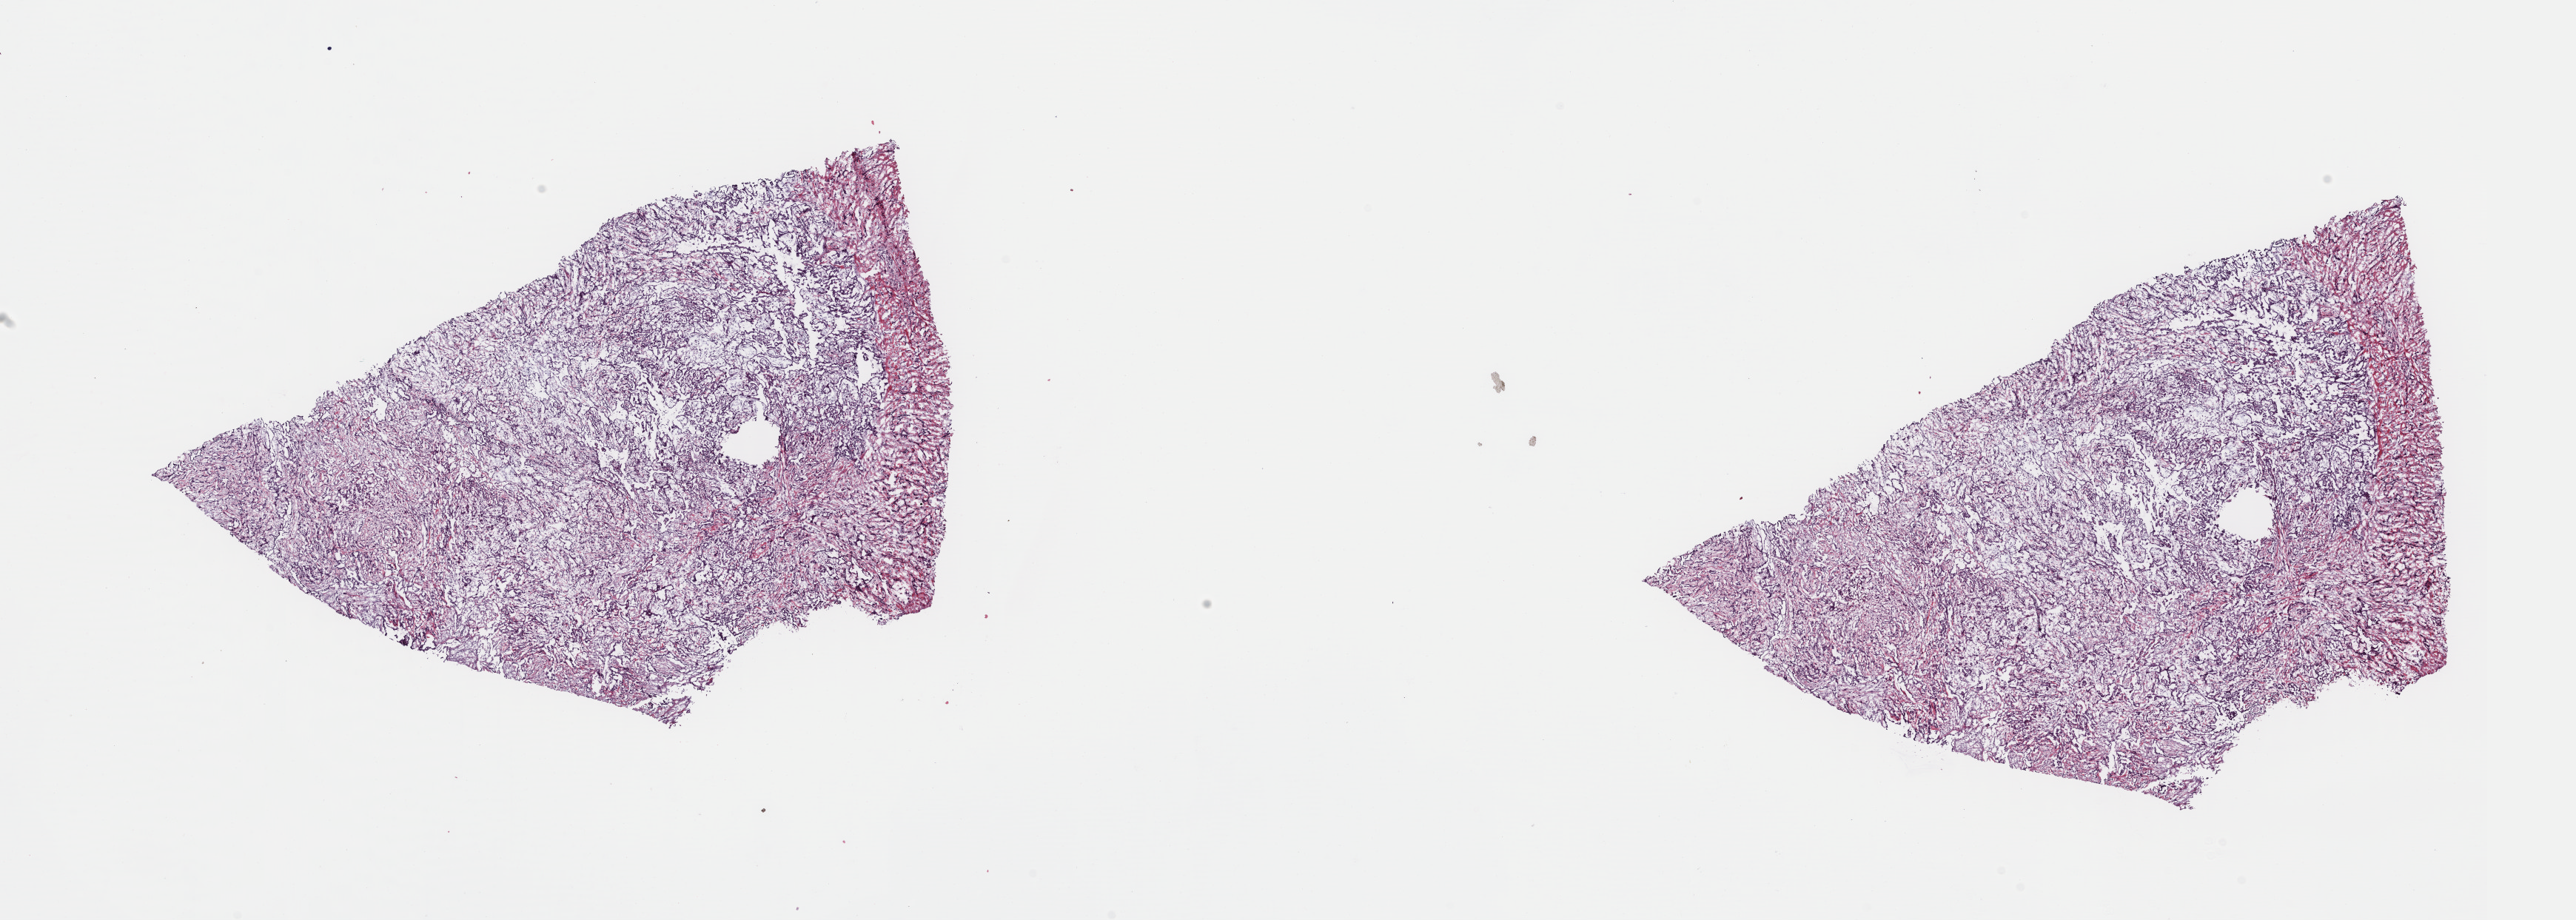
Digitized Hematoxylin and eosin (H&E) stained tissue section (whole slide) — whole scanned area (about 27.5 x 9.8 mm) shown as a low-resolution overview, frozen section from the top of the tissue portion, mesothelium, primary tumour sample. Female, age 66 years at initial diagnosis. Slide review estimates, as recorded: tumour cells 100%, tumour nuclei 70%.
Diagnosis: Mesothelioma, biphasic, malignant (pleura, NOS).